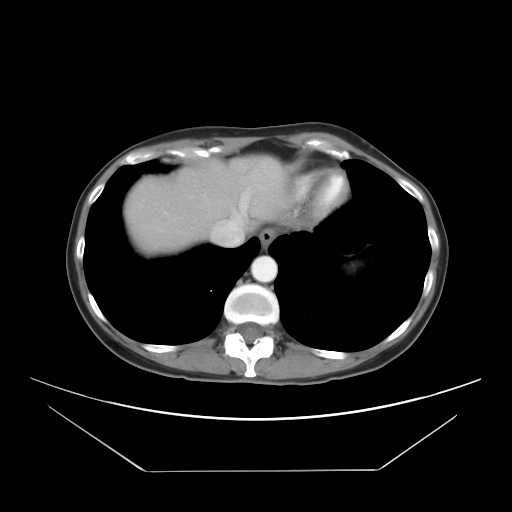
Contrast-enhanced abdominal CT, one axial slice; position 26 of 30 along the scan axis; reconstruction kernel STANDARD; 120 kVp; intravenous contrast given; soft-tissue window (W 400 / L 40 HU); 7.5 mm slice thickness; 512 × 512 image matrix, field of view 412 × 412 mm. Female patient, age 54 years. From the clinical record (not read from this slice): diagnosis: colorectal cancer liver metastases, imaged before liver resection; multiple liver metastases: yes; largest metastasis: 2.5 cm; chemotherapy before resection: no.
Annotated regions visible in this slice (expert manual segmentation):
- hepatic veins: box from (x=212, y=179) to (x=256, y=246) px
- liver: (x=129, y=157)–(x=286, y=250)
- planned liver remnant (the part of the liver to remain after resection): (x=129, y=162)–(x=270, y=251)